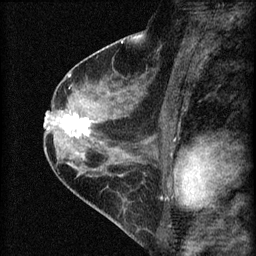
Breast MRI (dynamic contrast-enhanced), one sagittal slice; position 34 of 60 along the scan axis; dynamic contrast-enhanced series, image 2 of 4 at this slice position (ordered by acquisition); 1.5 T; TE 4.2 ms, TR 8.2 ms; 2 mm slice thickness; 256 × 256 image matrix. Patient: female, 45 years.
Structures marked on this image (semi-automatically segmented with operator editing):
- analysis volume of interest (the breast-tissue region the enhancement analysis was run in; not a lesion): bounding box (x1, y1, x2, y2) in pixels: (58, 107, 98, 147)
- tumour enhancement mask (voxels above the 70 % enhancement threshold inside the analysis volume of interest): (62, 114, 91, 139)